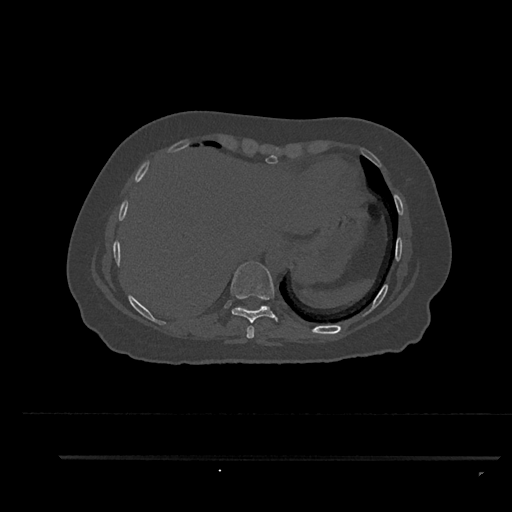
CT including the spine, one axial slice. Slice 410 of 797 in the series (ordered by position). Reconstruction kernel Br40s/3. Bone window (W 1800 / L 400 HU). 512 × 512 image matrix. Patient: female, 44 years. From the clinical record (not read from this slice): primary cancer: renal.
Structures marked on this image (semi-automatic segmentation, software-assisted and operator-edited):
- T8 vertebra: bounding box (x1, y1, x2, y2) in pixels: (246, 326, 255, 339)
- T9 vertebra: (231, 262, 278, 323)